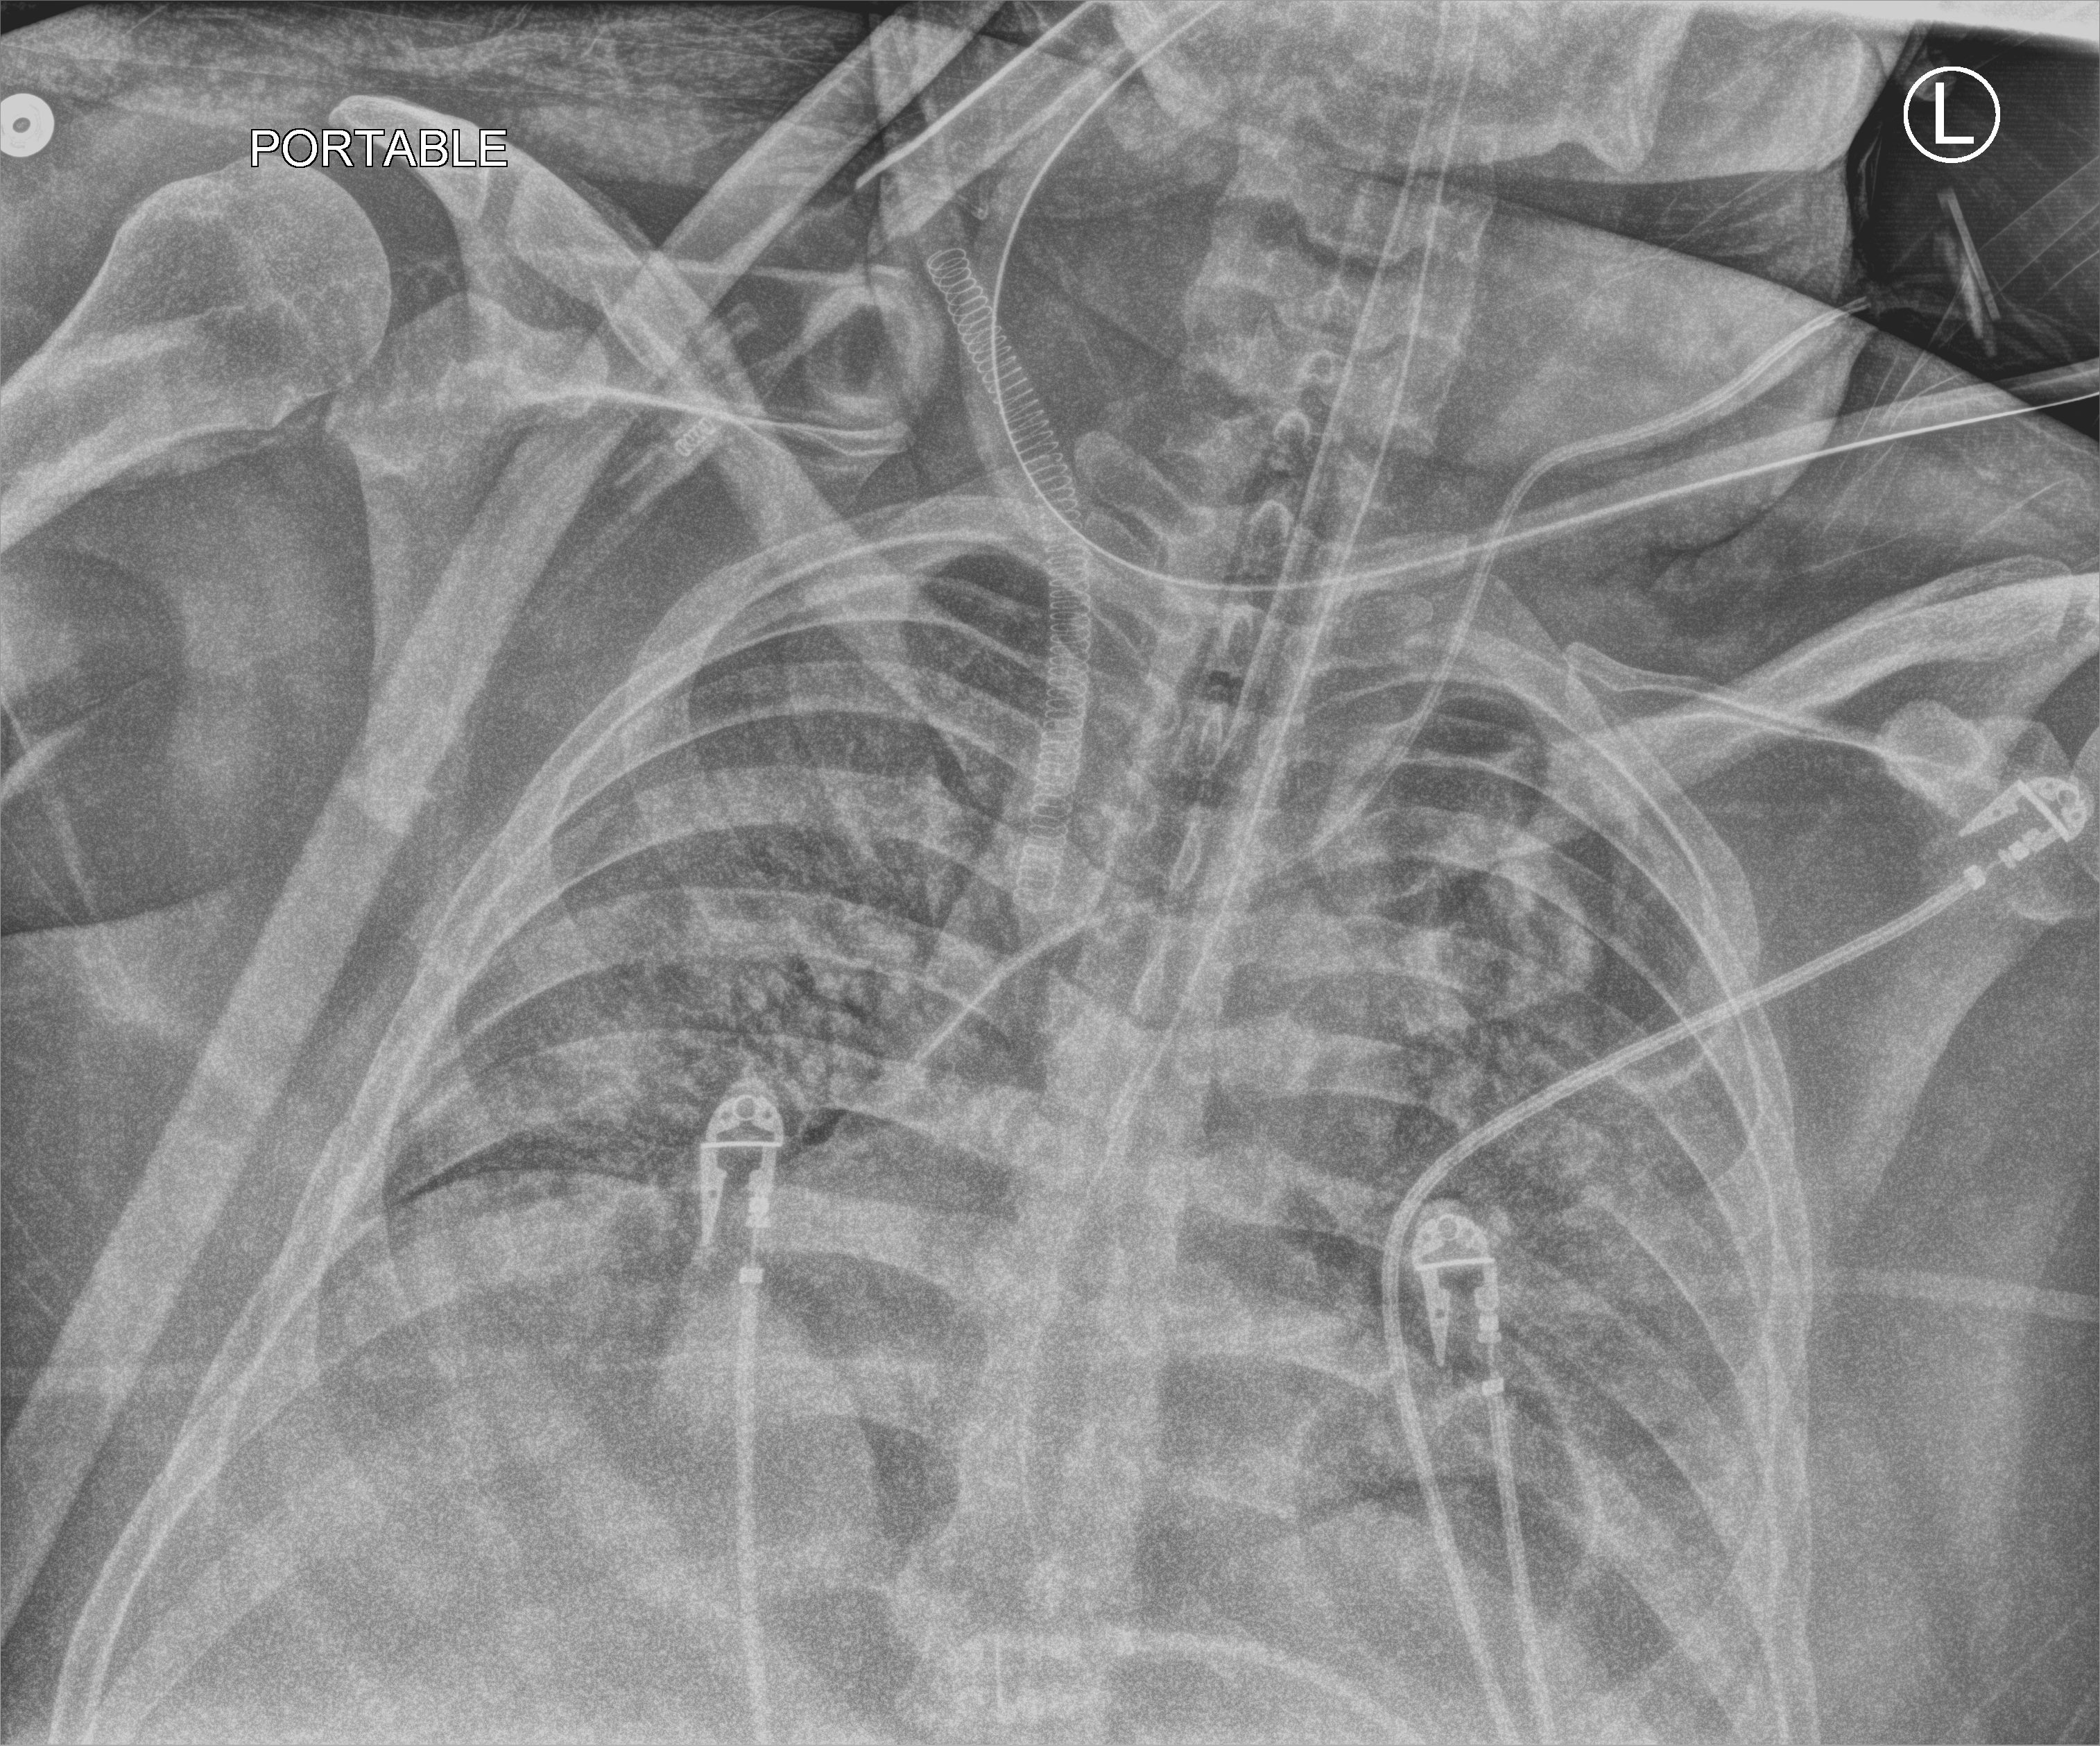
Portable chest radiograph, anteroposterior (AP) projection. Adult patient hospitalised with COVID-19, age 18–59 years.
From the hospital-stay record, not from the radiograph (when in the stay this image was taken is not recorded): mechanically ventilated during this hospital stay: yes.